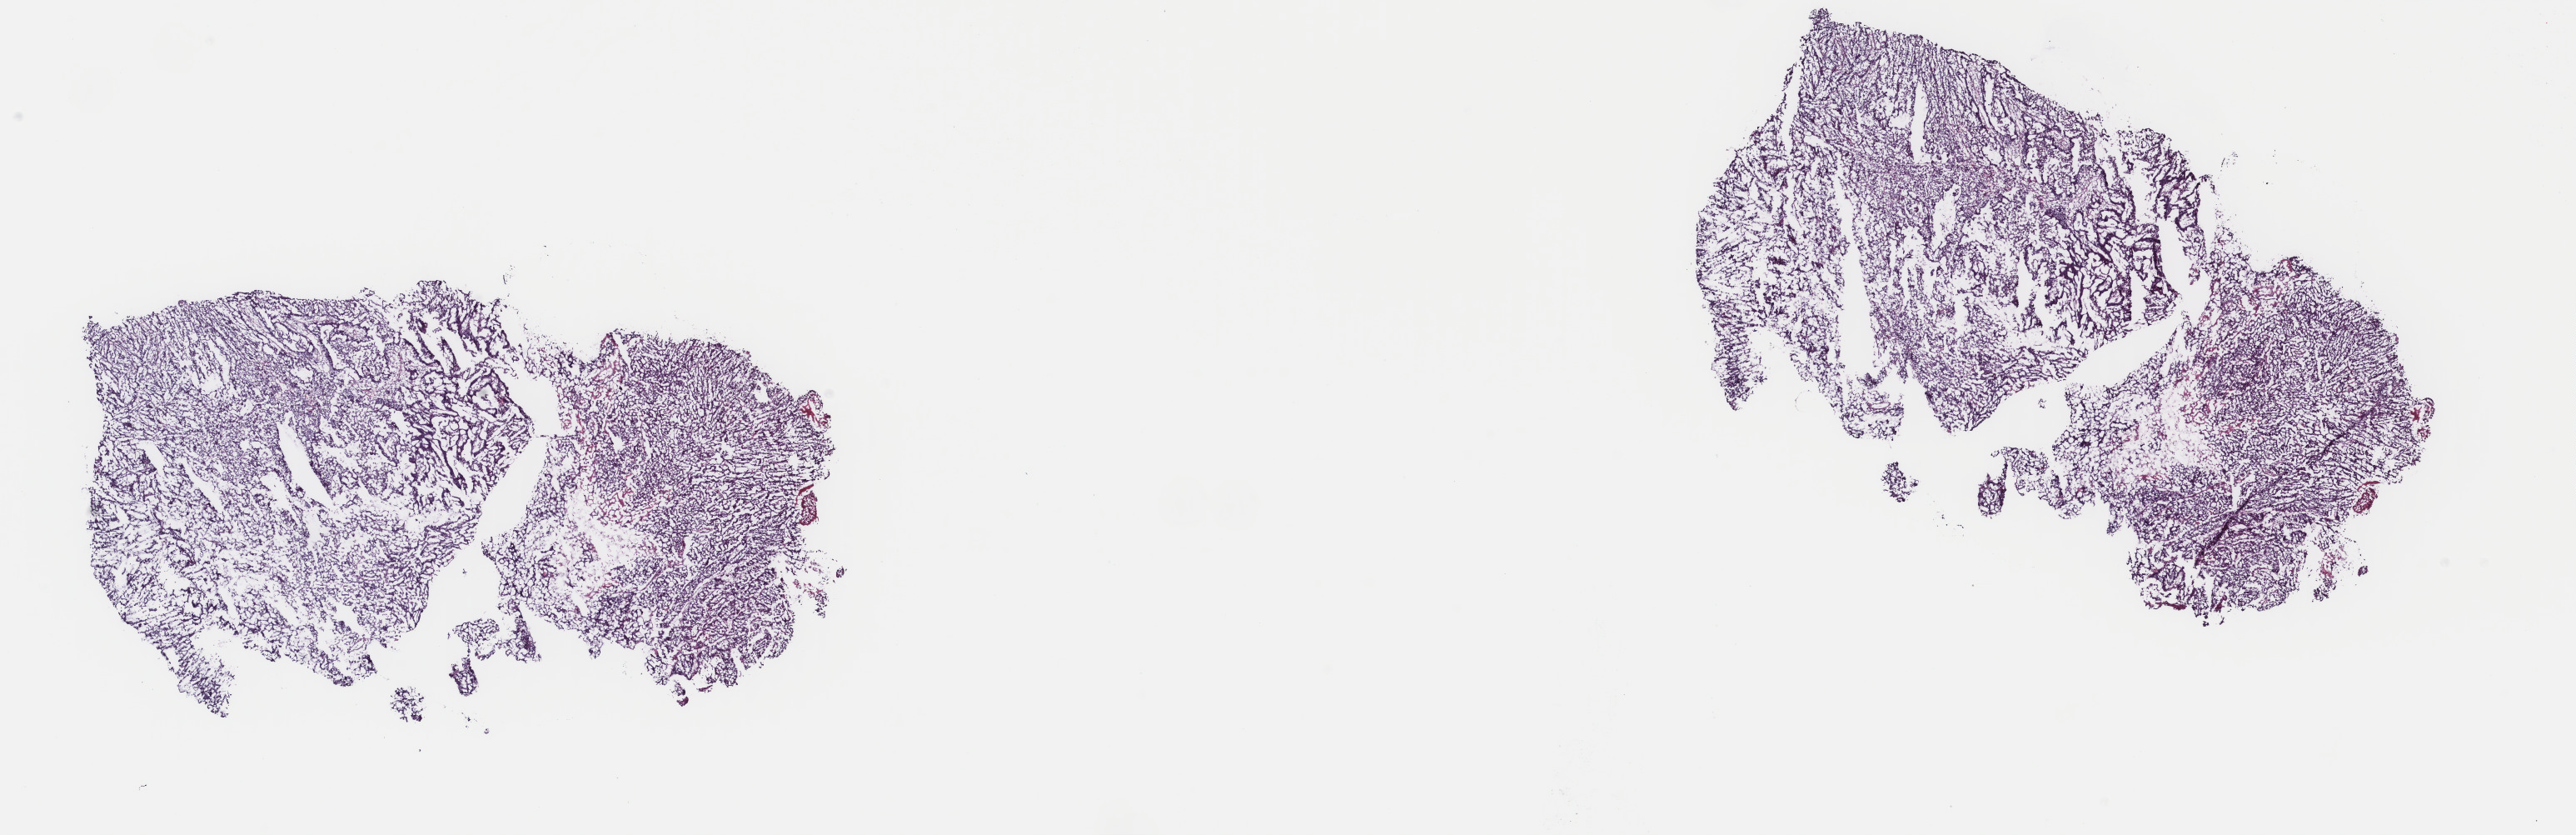
Digitized Hematoxylin and eosin (H&E) stained tissue section (whole slide) — shown as a low-resolution overview of the whole scanned area (about 24.6 x 8.0 mm). Frozen section from the top of the tissue portion. Bladder, primary tumour sample. Patient: male, age at initial diagnosis 59 years. Histologic grade: high grade. Pathologist review of this section (percent, as recorded): tumour cells 95%, tumour nuclei 90%, normal cells 0%, stromal cells 0%, necrosis 5%. Inflammatory infiltration, as recorded: lymphocyte infiltration 2%, monocyte infiltration 0%, neutrophil infiltration 0%.
Lymph nodes positive (case pathology): 0 of 27 examined. Pathologic diagnosis: Transitional cell carcinoma. AJCC pathologic stage: III (7th edition).